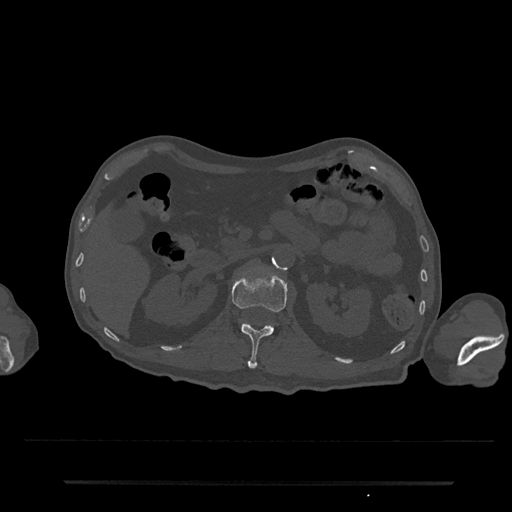
CT including the spine, one axial slice. Position 116 of 797 along the scan axis. Bone window (W 1800 / L 400 HU). 512 × 512 image matrix, field of view 427 × 427 mm. Male patient, age 74 years. From the clinical record (not read from this slice): primary cancer: prostate.
Structures marked on this image (semi-automatic segmentation, software-assisted and operator-edited):
- L1 vertebra: bounding box <232,268,287,369> (left, top, right, bottom; pixels)